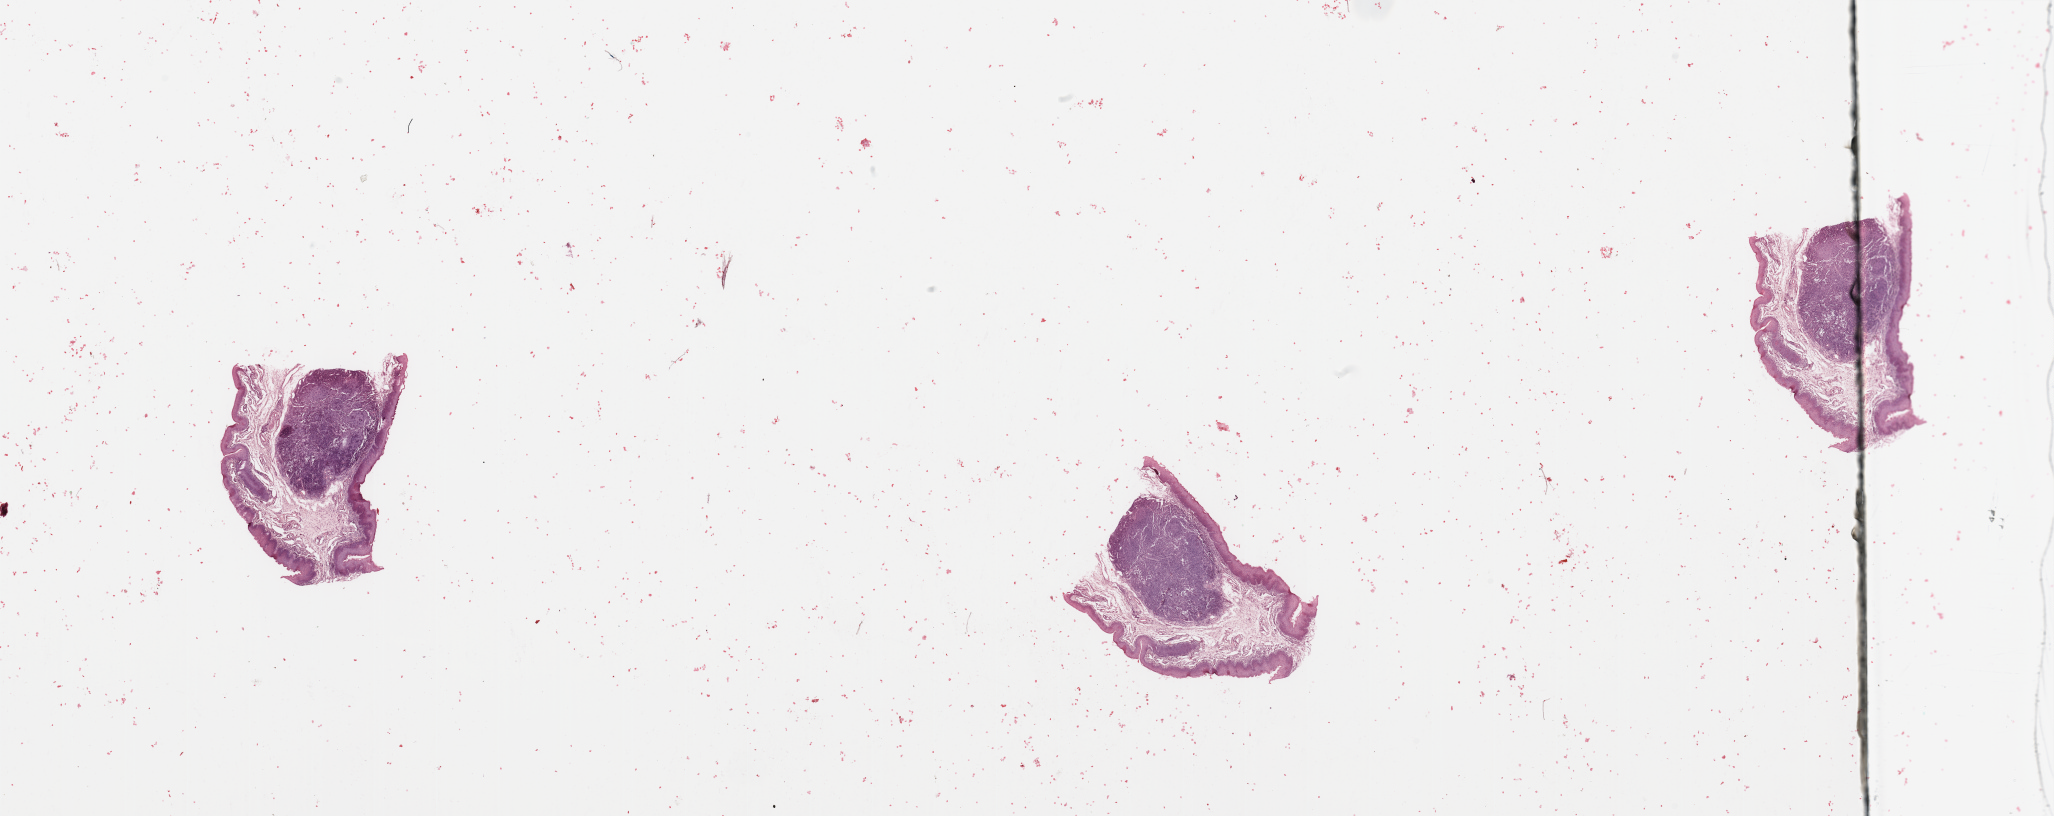
H&E-stained whole-slide image, low-resolution overview of the scanned area, about 32.5 x 12.9 mm (from a 20x scan), normal (non-tumour) tissue sample, head and neck. Male, 56 y/o.
This section: normal (non-tumour) tissue from the same patient. Patient diagnosis: Squamous cell carcinoma, NOS (larynx, NOS).